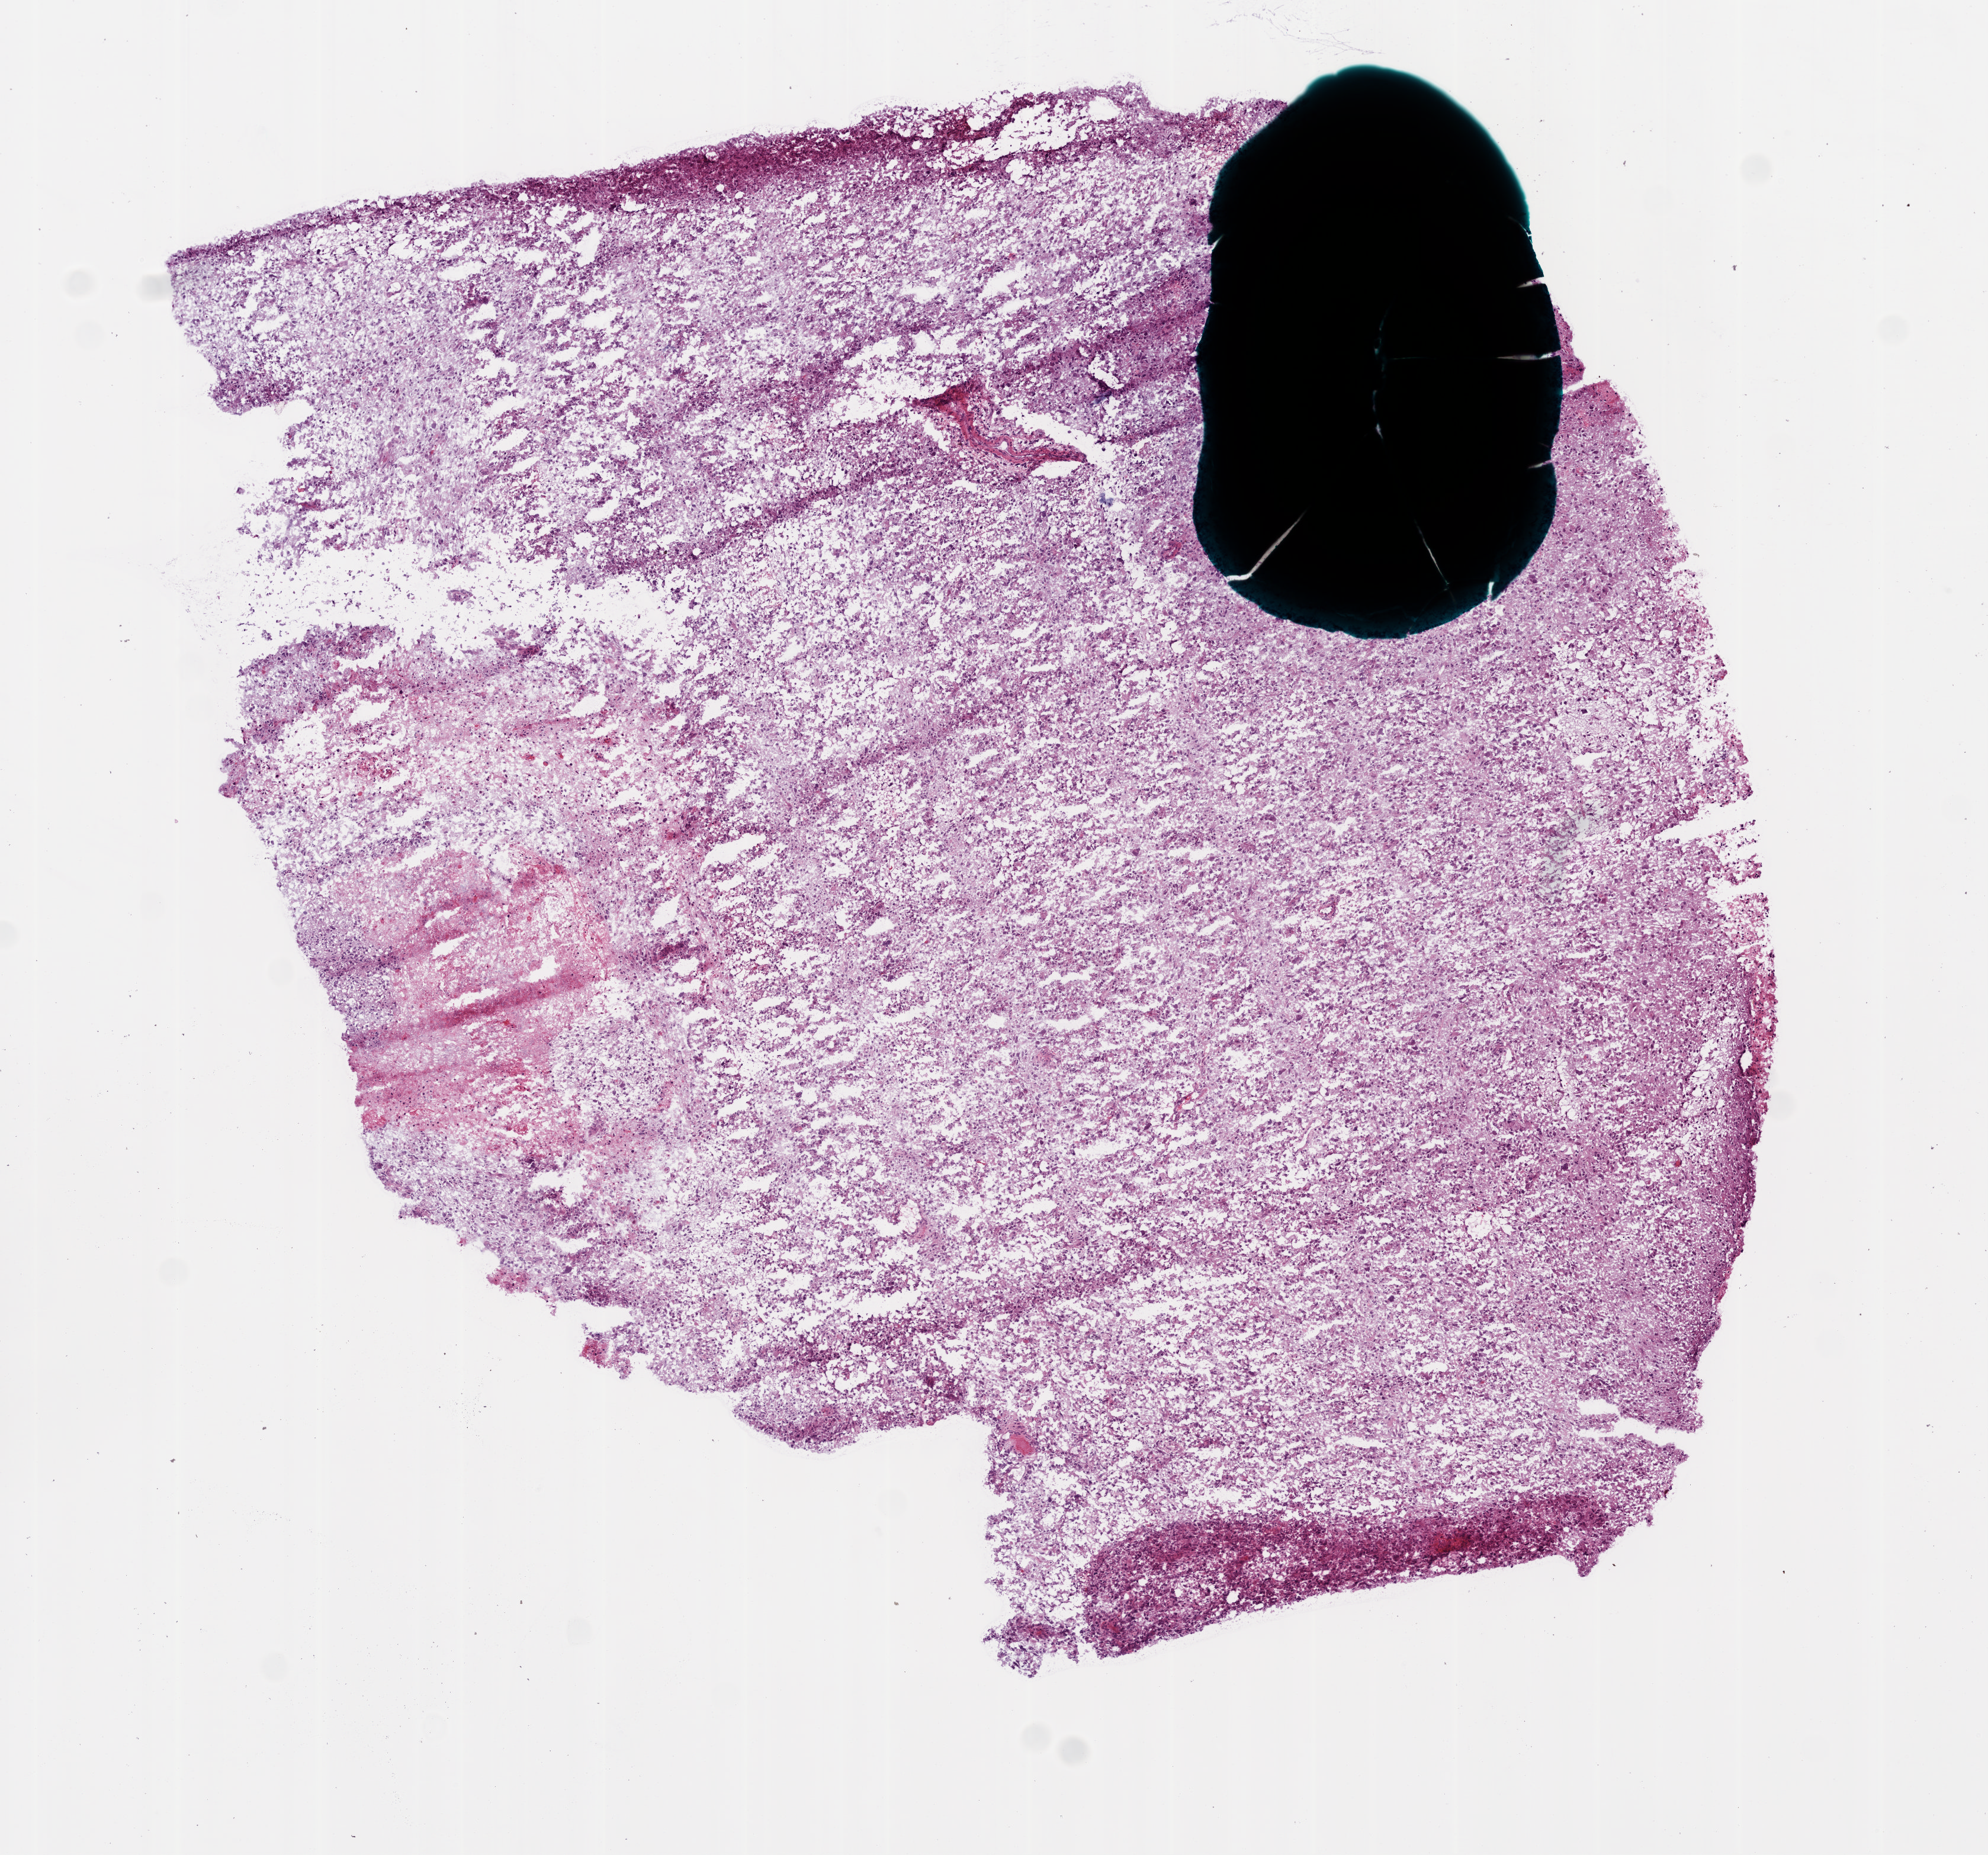
Digitized H&E-stained tissue section (whole slide), low-resolution overview of the scanned area, about 6.8 x 6.3 mm, frozen section from the bottom of the tissue portion, sample: primary tumour, brain. Male, age 58 years at initial diagnosis.
Diagnosis: Glioblastoma.